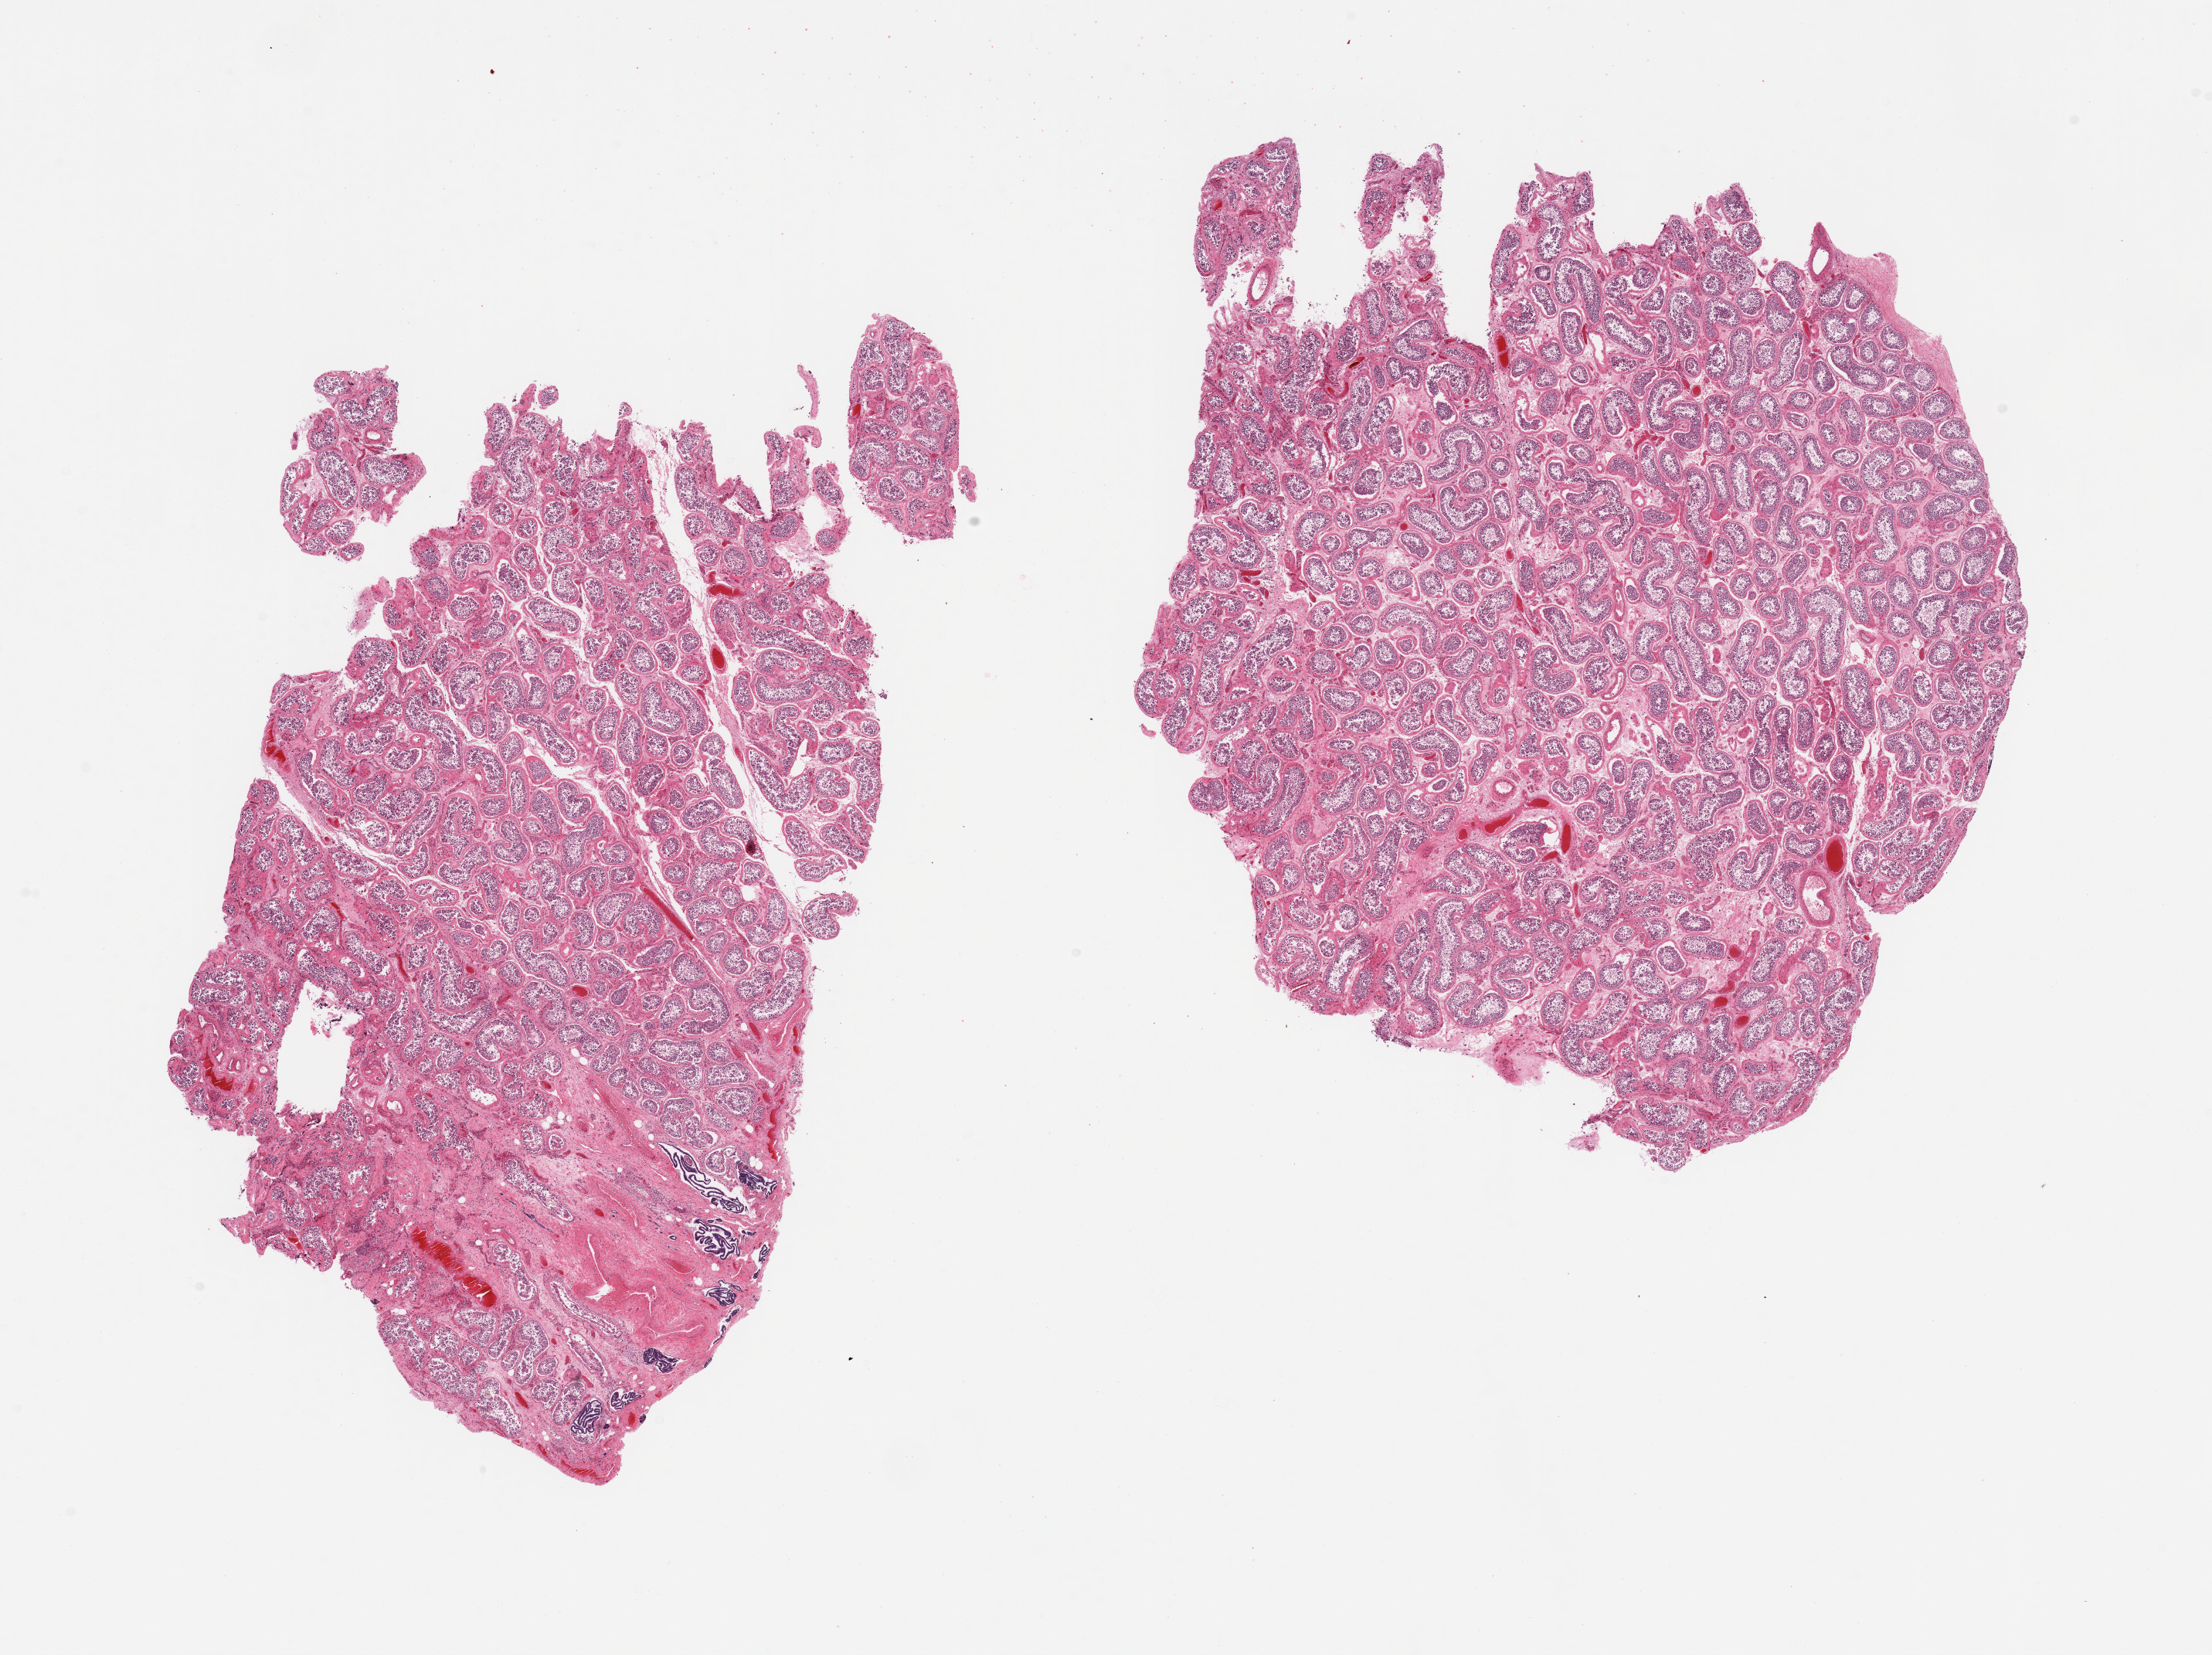
H&E whole-slide image, shown as a low-resolution overview of the whole scanned area (about 22.6 x 16.9 mm). PAXgene-fixed, paraffin-embedded tissue. Sampled site (target tissue): testis. Tissue donor sample. Donor sex: male.
Review note (as recorded): 2 pieces; active spermatogenesis; rete testis sampled in 1 piece [10%].